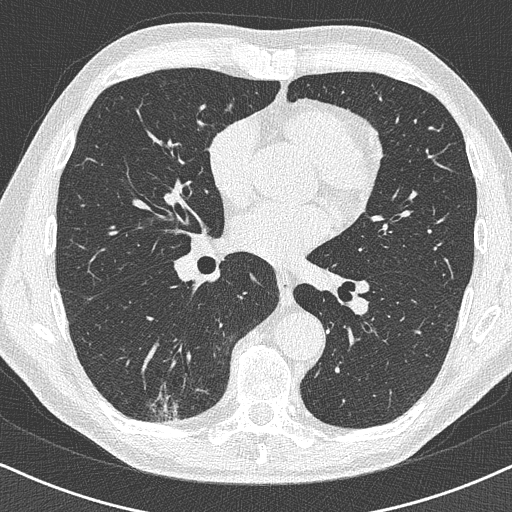
Axial slice from a low-dose chest CT screening exam; baseline annual screen; lung window (W 1500 / L -600 HU); 1 mm slice thickness; 120 kVp. Male, age 63 years at enrolment. Former smoker at enrolment.
- Expert-annotated lung lesion, bounding box [x1, y1, x2, y2] px = [128, 358, 200, 427].
- The exam's reader record, not a measurement of the box and not confirmed to be the same lesion: non-calcified nodule or mass ≥4 mm, right lower lobe, 16 × 13 mm, poorly defined margins.
- Later outcome: lung cancer diagnosed 74 days after this screen — adenocarcinoma, NOS, right lower lobe, moderately differentiated (G2), stage IA (AJCC 6th edition), 20 mm at pathology.